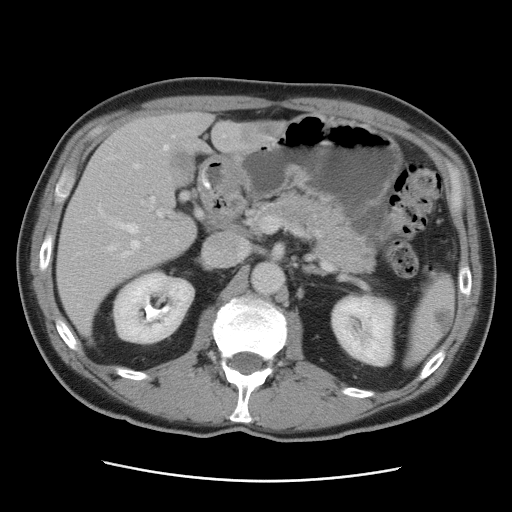
Contrast-enhanced abdominal CT, one axial slice; slice 49 of 89 in the series (ordered by position); 120 kVp; soft-tissue window (W 400 / L 40 HU); 5 mm slice thickness; 512 × 512 image matrix. Male patient, age 59 years. Case-level facts recorded for this patient, not image findings: diagnosis: colorectal cancer liver metastases, imaged before liver resection; multiple liver metastases: yes; largest metastasis: 0.6 cm.
Annotated regions visible in this slice (expert manual segmentation):
- hepatic veins: bounding box (x1, y1, x2, y2) in pixels: (98, 135, 226, 257)
- liver: (56, 113, 288, 340)
- planned liver remnant (the part of the liver to remain after resection): (71, 113, 213, 244)
- portal vein (with intrahepatic branches): (142, 197, 178, 243)
- liver metastasis: (241, 125, 284, 140)